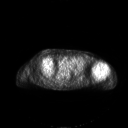
FDG PET of an extremity soft-tissue mass (from a PET/CT study), one axial slice. Position 151 of 267 along the scan axis. 3.27 mm slice thickness. 128 × 128 image matrix, field of view 700 × 700 mm. Female patient, age 83 years. Case-level facts recorded for this patient, not image findings: histological type: pleiomorphic leiomyosarcoma; grade: high; site of the primary tumour: left biceps.
Structures marked on this image (expert contour drawn on MRI and transferred to this co-registered scan by the dataset authors):
- gross tumour volume including surrounding oedema: bounding box (x1, y1, x2, y2) in pixels: (91, 62, 107, 77)
- gross tumour volume (mass): (91, 62, 107, 77)